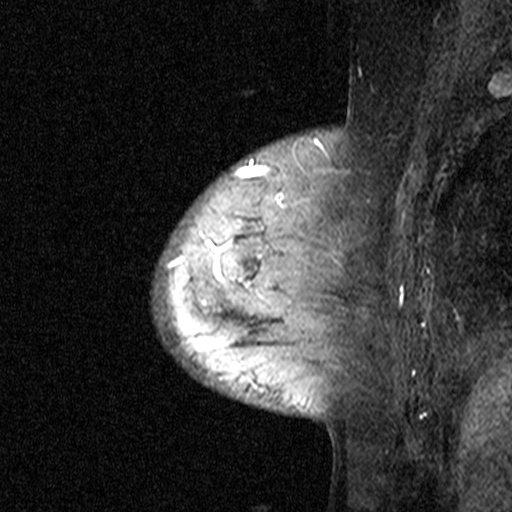
Breast MRI (dynamic contrast-enhanced), one sagittal slice; slice 8 of 44 in the series (ordered by position); dynamic contrast-enhanced study with each time point stored as its own series, time point 3 of 4 at this slice position (ordered by acquisition time); 1.5 T; TE 4.5 ms, TR 11 ms; 512 × 512 image matrix, field of view 200 × 200 mm. Patient: female, 65 years. Case-level facts recorded for this patient, not image findings: setting: breast cancer imaged before/during neoadjuvant chemotherapy; receptor status: HER2-positive.
Structures marked on this image (semi-automatically segmented with operator editing):
- analysis volume of interest (the breast-tissue region the enhancement analysis was run in; not a lesion): bounding box <182,190,353,361> (left, top, right, bottom; pixels)
- tumour enhancement mask (voxels above the 90 % enhancement threshold inside the analysis volume of interest): <182,242,251,287>